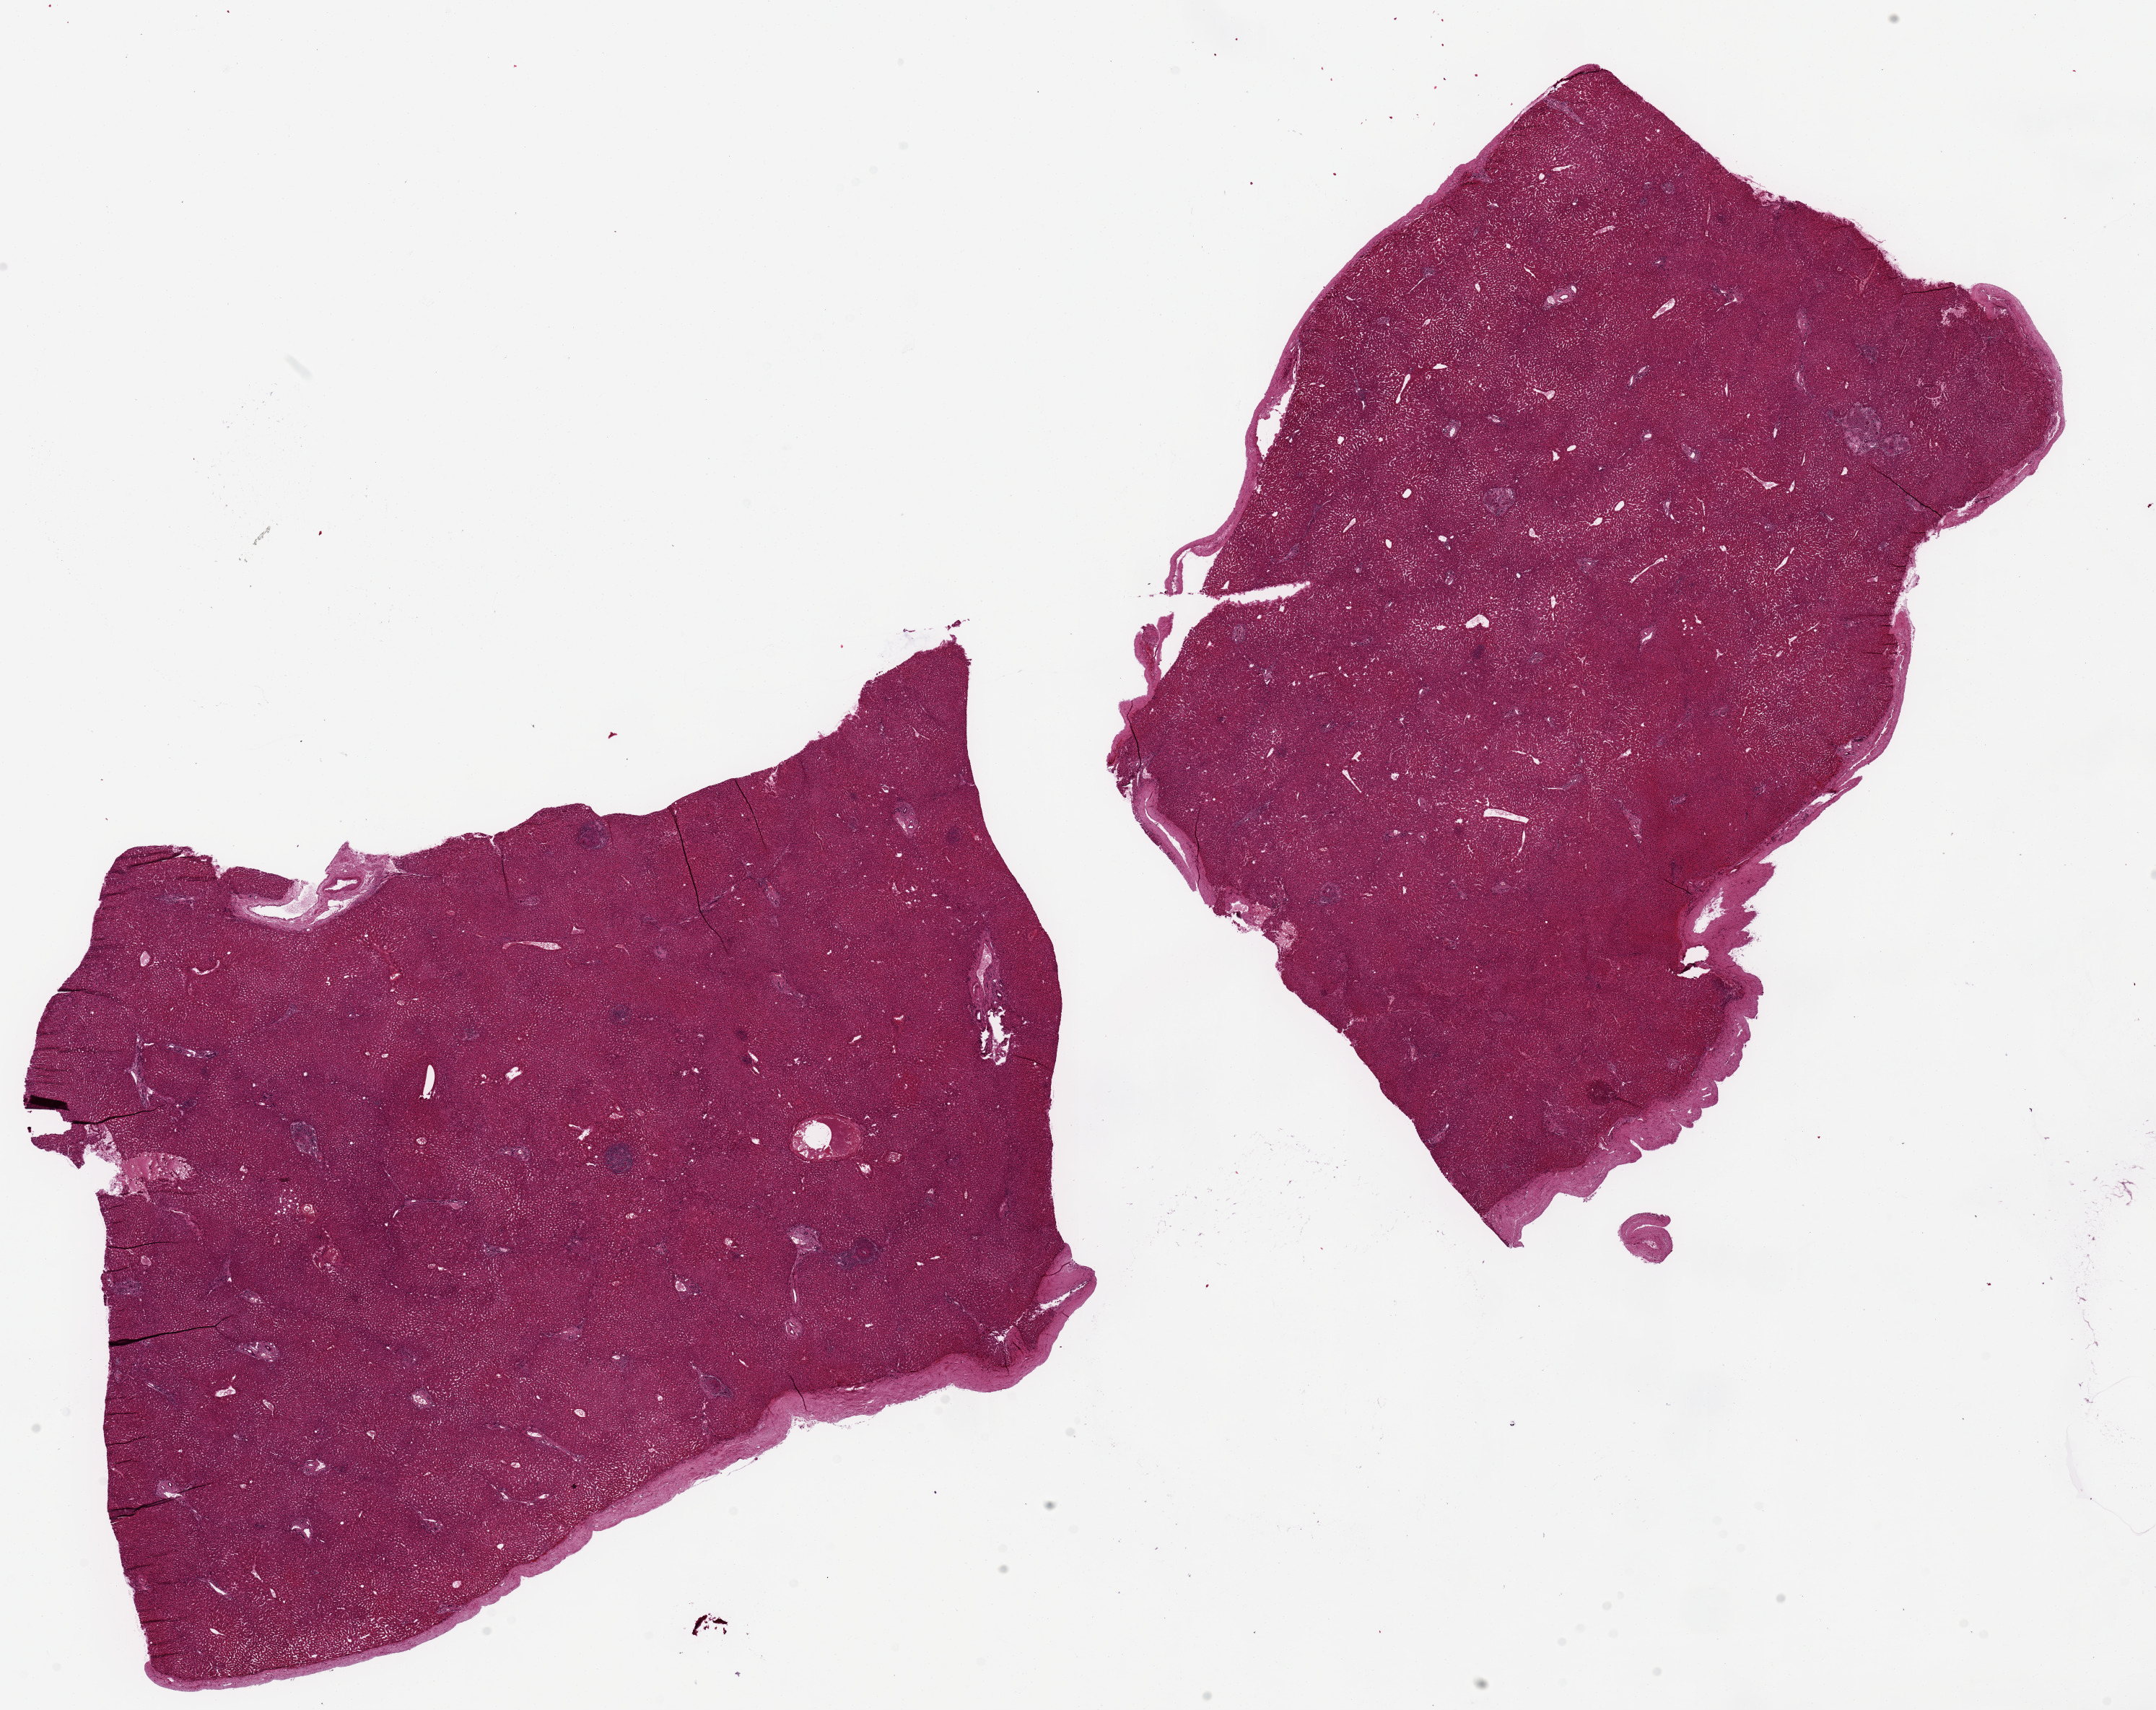
Whole-slide image, H&E stain, a low-resolution overview of the entire scanned area, about 23.6 x 18.7 mm, PAXgene-fixed paraffin-embedded (PFPE) section, section of liver (target tissue), tissue donor sample.
Reviewer comment on this tissue sample: 2 pieces, 11x9 & 12x9mm; giant cell granulomas (history of sarcoid); capsule present up to 0.4mm thick, specimen should be sampled below capsule.